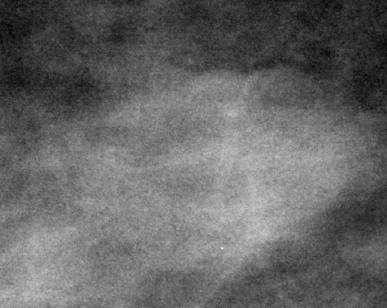
Cropped region of a digitized screen-film mammogram centred on a radiologist-marked abnormality; right breast; MLO view; BI-RADS breast density category 2 (scale 1–4).
Marked abnormality: mass, shape lobulated, margins microlobulated; BI-RADS assessment category 3; subtlety rating 5 on a 1 (subtle) to 5 (obvious) scale; pathology (as recorded): benign.